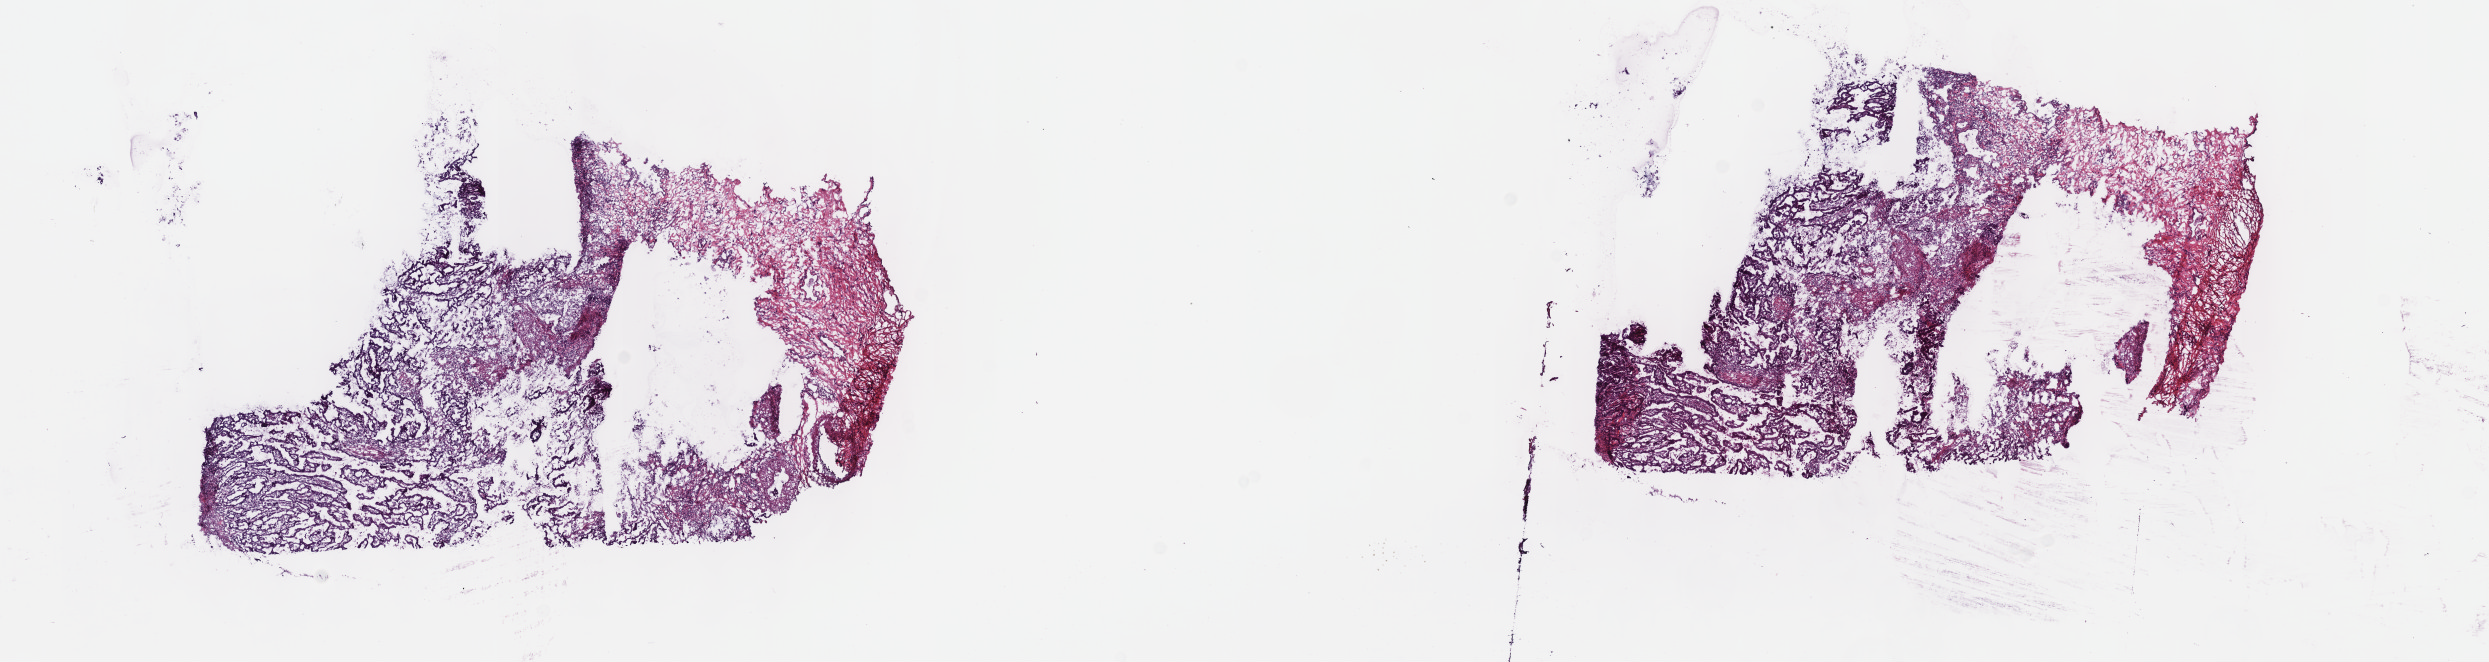
H&E whole-slide image, whole scanned area (about 20.1 x 5.4 mm, slide scanned at 40x) shown as a low-resolution overview, frozen section, stomach, primary tumour sample. Male, age 72 years at initial diagnosis. Histologic grade: G2 (moderately differentiated). Composition of this section per pathologist review: tumour cells 60%, tumour nuclei 70%, normal cells 20%, stromal cells 20%, necrosis 0%. Inflammatory infiltration, as recorded: lymphocyte infiltration 0%, monocyte infiltration 0%, neutrophil infiltration 0%.
• diagnosis: Tubular adenocarcinoma (body of stomach)
• lymph nodes positive (case pathology): 1 of 14 examined
• AJCC pathologic stage: IIIA (7th edition)